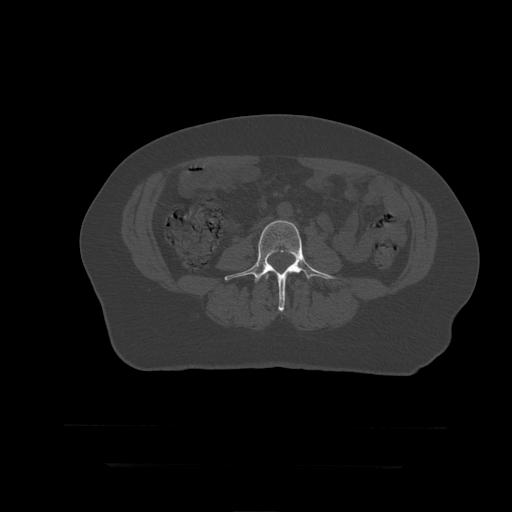
CT including the spine, one axial slice. Position 101 of 399 along the scan axis. Bone window (W 1800 / L 400 HU). 1.25 mm slice thickness. 512 × 512 image matrix, field of view 450 × 450 mm. Patient age 41 years. Case-level facts recorded for this patient, not image findings: primary cancer: breast.
Annotated regions visible in this slice (semi-automatically segmented with operator editing):
- L3 vertebra: bounding box [x1, y1, x2, y2] px = [266, 274, 269, 280]
- L4 vertebra: [225, 221, 337, 312]